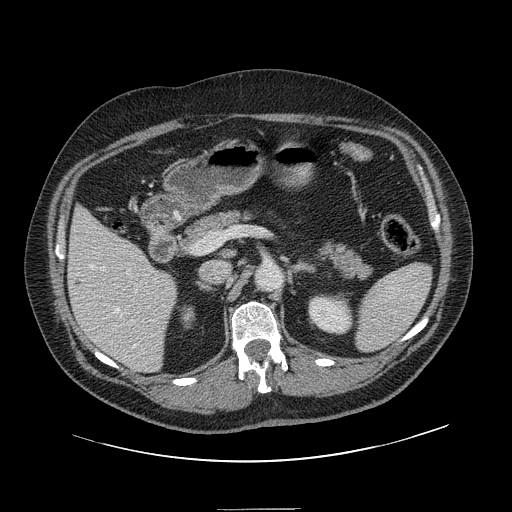
Contrast-enhanced abdominal CT, one axial slice. Slice 72 of 154 in the series (ordered by position). 120 kVp. Intravenous contrast given. Soft-tissue window (W 400 / L 40 HU). 2.5 mm slice thickness. 512 × 512 image matrix, field of view 451 × 451 mm. Male patient, age 61 years. Case-level facts recorded for this patient, not image findings: diagnosis: colorectal cancer liver metastases, imaged before liver resection; multiple liver metastases: yes; largest metastasis: 2.6 cm; disease in both lobes: yes.
Structures marked on this image (expert manual segmentation):
- hepatic veins: bounding box <90,265,137,349> (left, top, right, bottom; pixels)
- liver: <69,209,177,371>
- planned liver remnant (the part of the liver to remain after resection): <70,209,177,366>
- portal vein (with intrahepatic branches): <131,307,149,321>
- liver metastasis: <77,282,82,288>